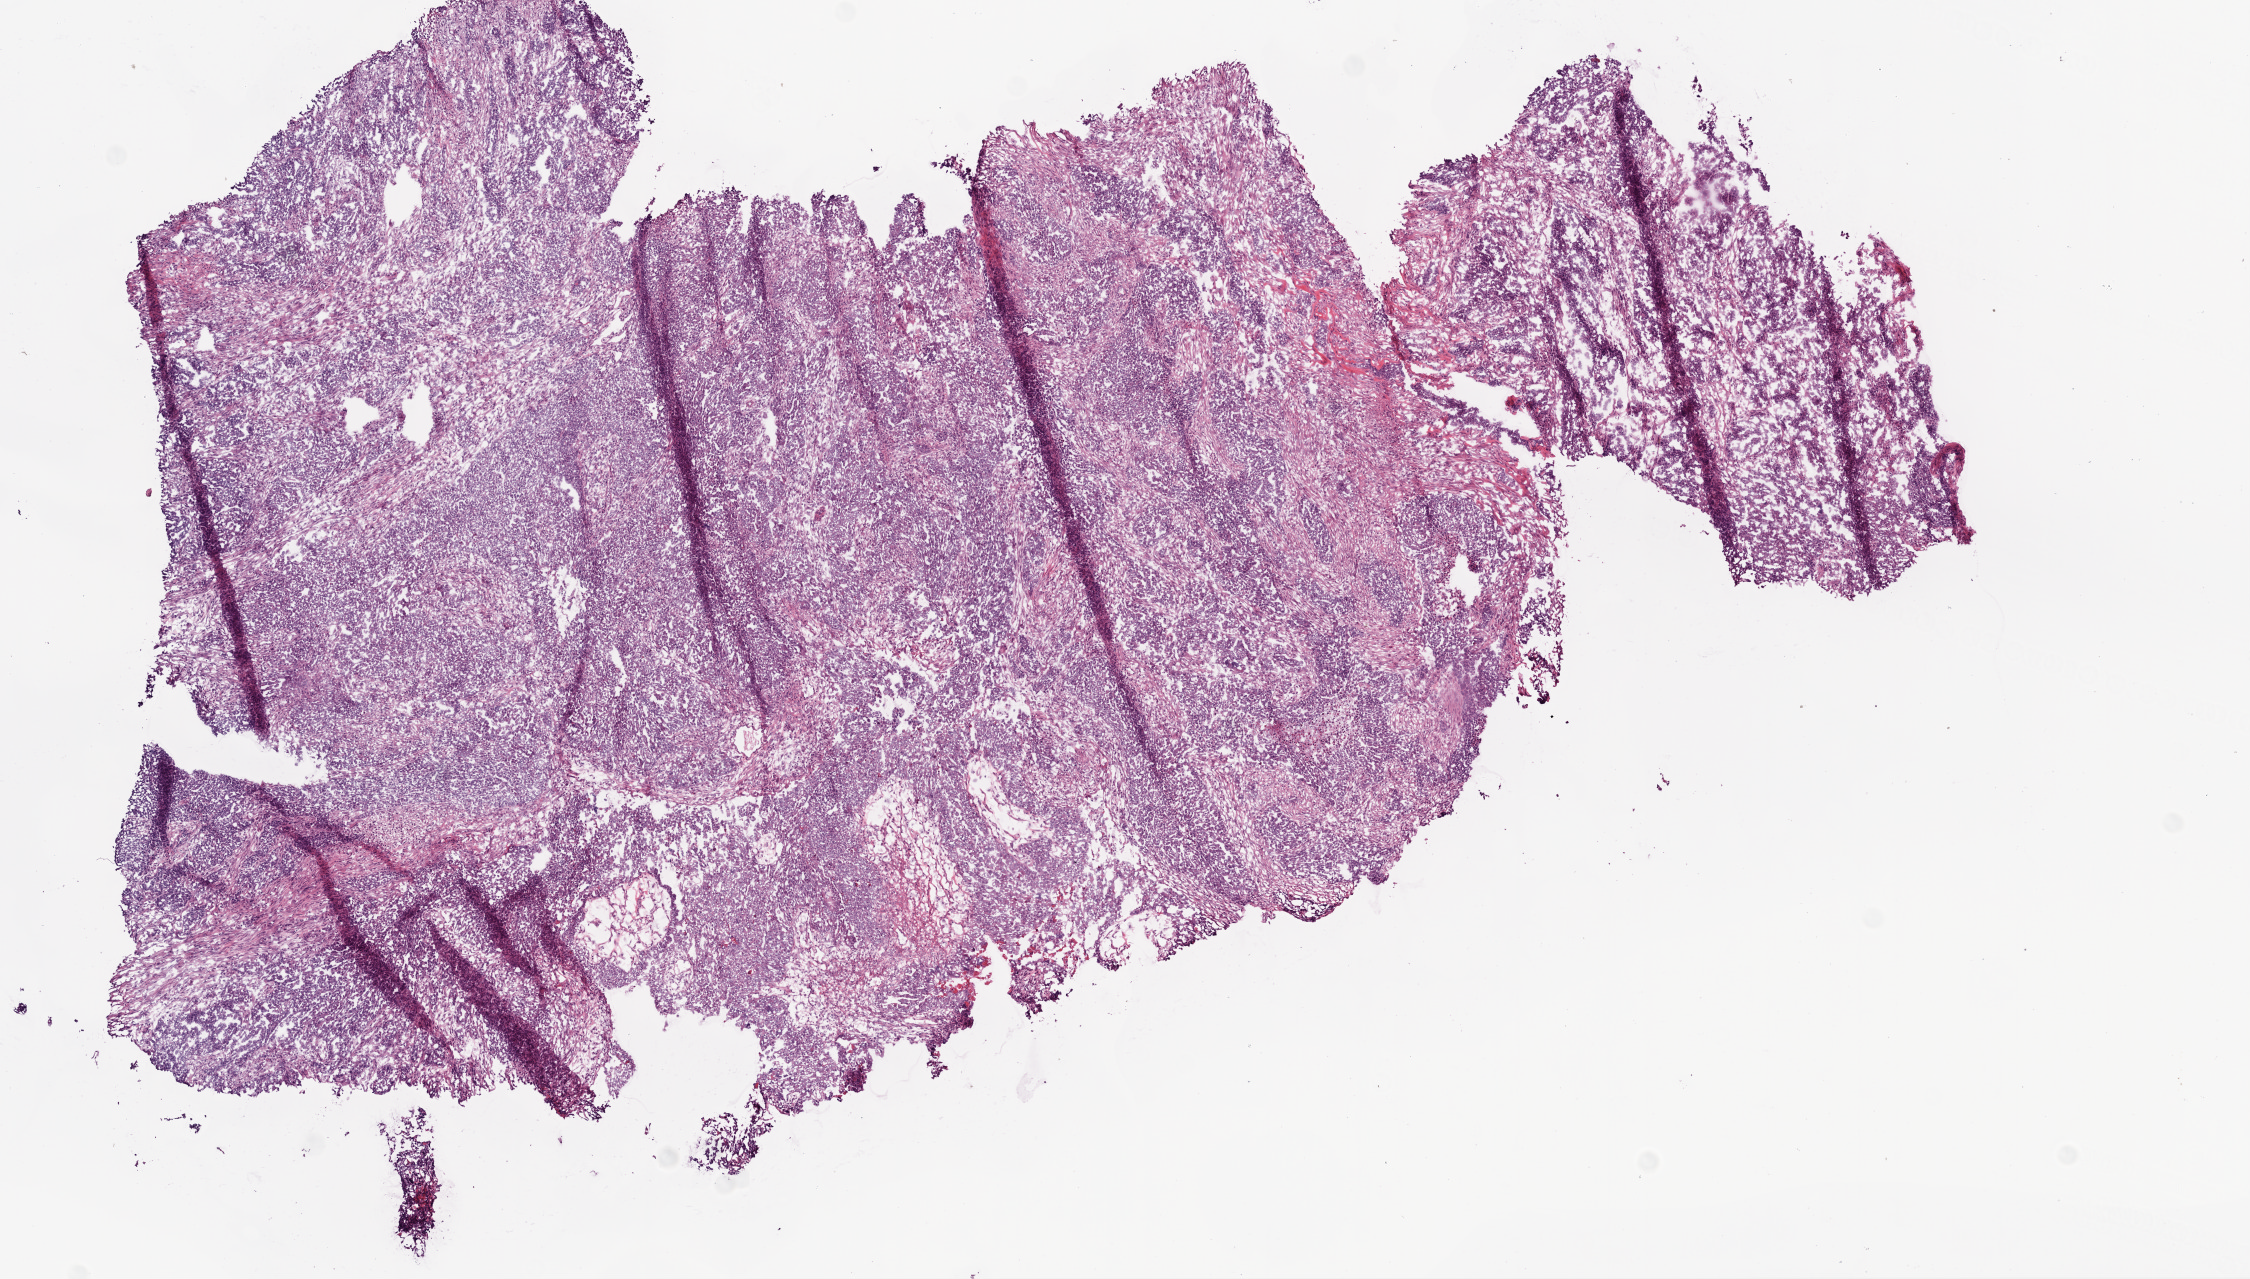
Whole-slide histology image, H&E-stained — shown as a low-resolution overview of the whole scanned area (about 9.0 x 5.1 mm, acquisition: 20x scan); frozen section from the bottom of the tissue portion; ovary, primary tumour sample. Patient: female, age at initial diagnosis 42 years. Histologic grade: G3 (poorly differentiated). Composition of this section per pathologist review: tumour cells 95%, tumour nuclei 85%, normal cells 0%, stromal cells 0%, necrosis 5%. Infiltration values recorded for this section: lymphocyte infiltration 5%.
FIGO stage: IV. Laterality: bilateral. Histologic diagnosis: Serous cystadenocarcinoma, NOS.